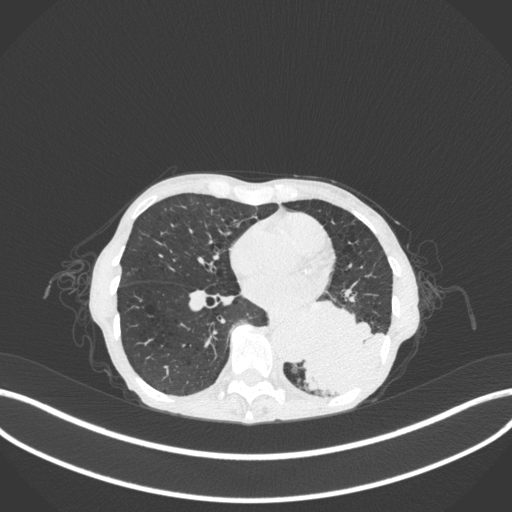
Chest CT, one axial slice. Slice 112 of 347 in the series (ordered by position). Reconstruction kernel B31f. Lung window (W 1500 / L -600 HU). 512 × 512 image matrix. Female patient, age 70 years. Case-level facts recorded for this patient, not image findings: clinical TNM (as recorded): T3 N0 M0; histopathological grade: G3.
Structures marked on this image (rectangle marked by the reading radiologist):
- lung tumour (recorded histology: small cell carcinoma): bounding box [x1, y1, x2, y2] px = [303, 289, 386, 398]